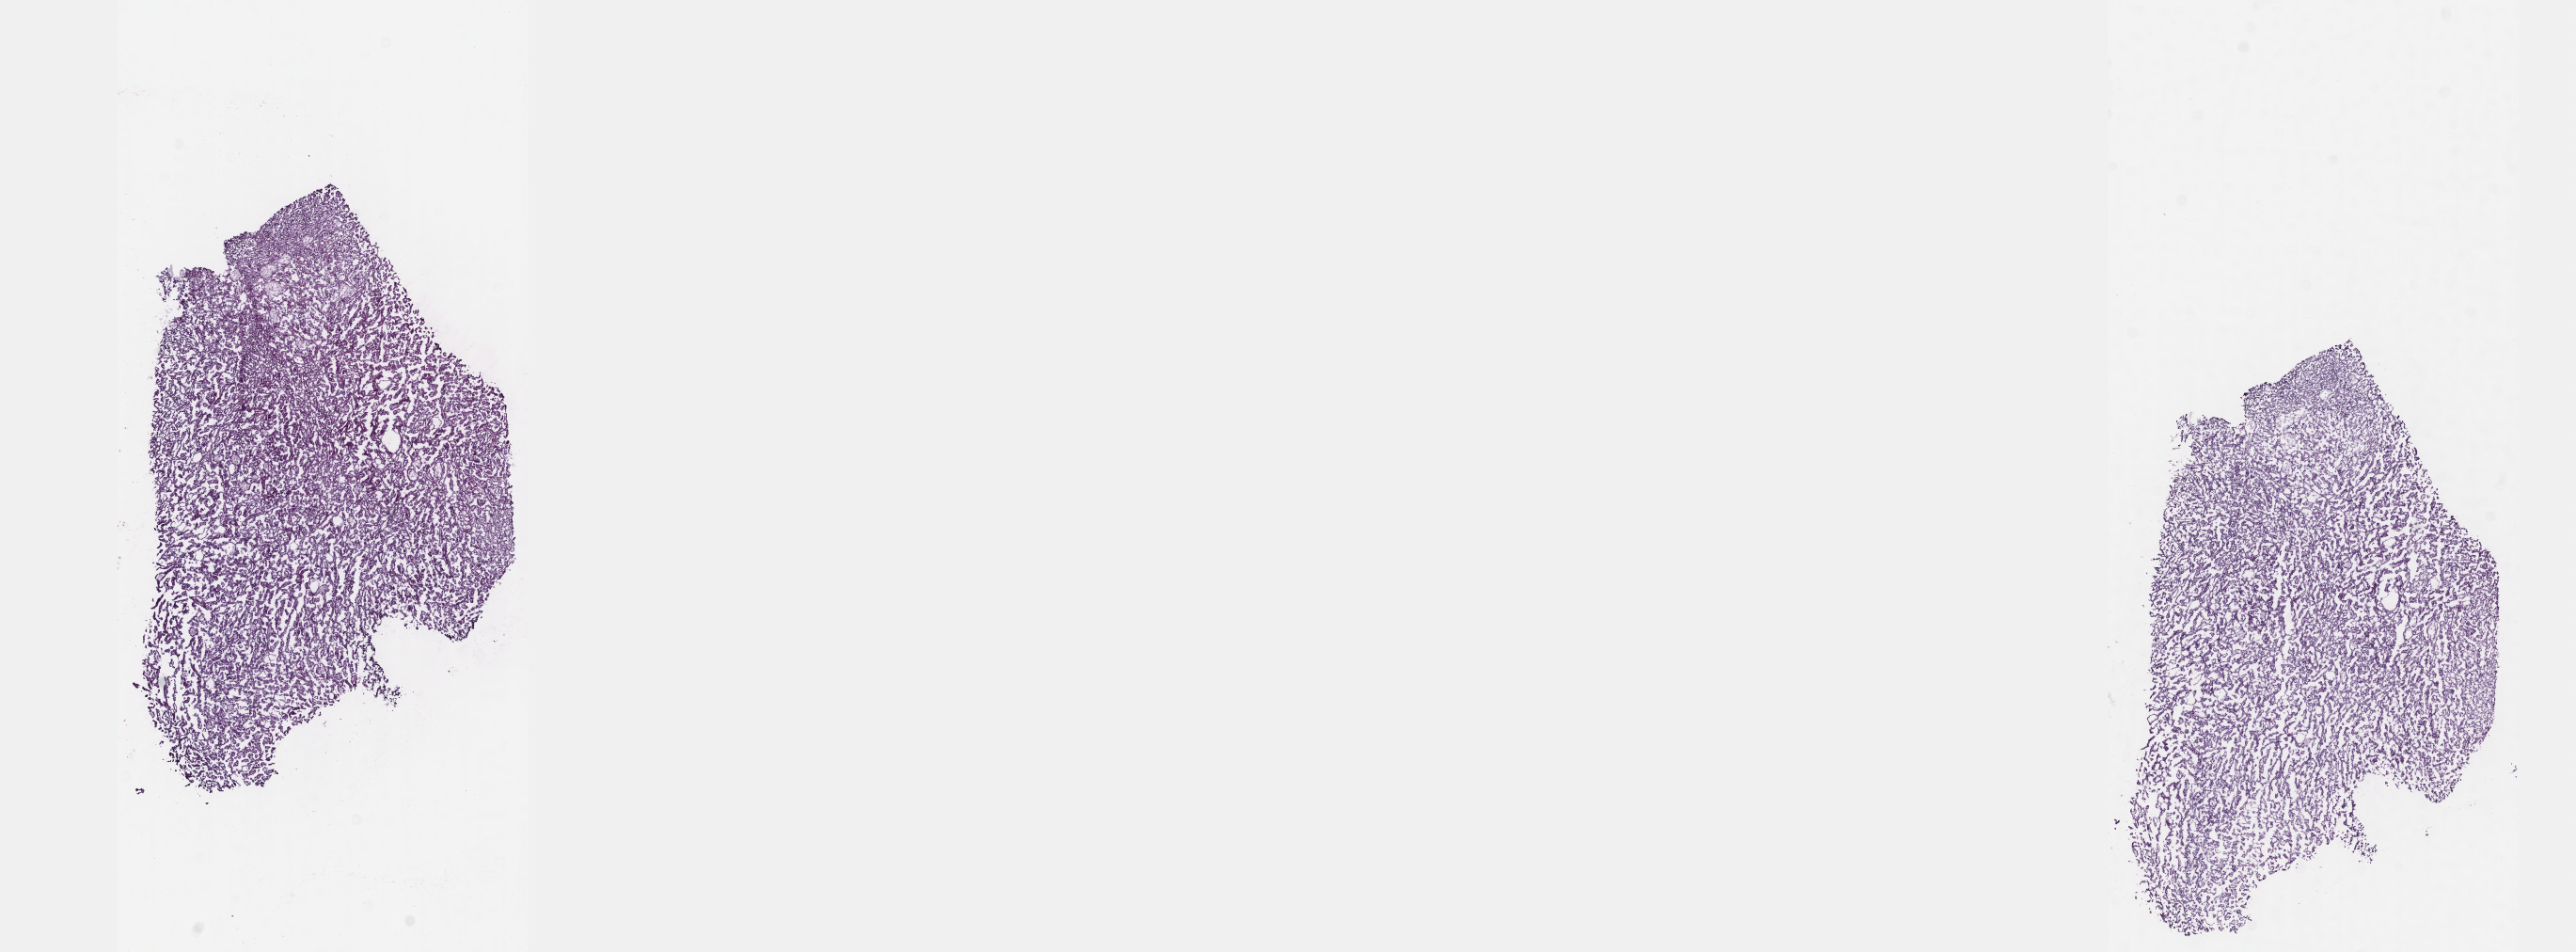
H&E whole-slide image — shown as a low-resolution overview of the whole scanned area (about 22.1 x 8.2 mm, acquisition: 40x scan). Frozen section. Sample: primary tumour, kidney. Male patient; age at initial diagnosis 47 years. Pathologist review of this section (percent, as recorded): tumour cells 90%, tumour nuclei 95%, normal cells 0%, stromal cells 10%, necrosis 0%. Inflammatory infiltration, as recorded: lymphocyte infiltration 0%, monocyte infiltration 0%, neutrophil infiltration 0%.
TNM: T1 NX M0. Pathologic diagnosis: Papillary adenocarcinoma, NOS. AJCC pathologic stage: I (7th edition).